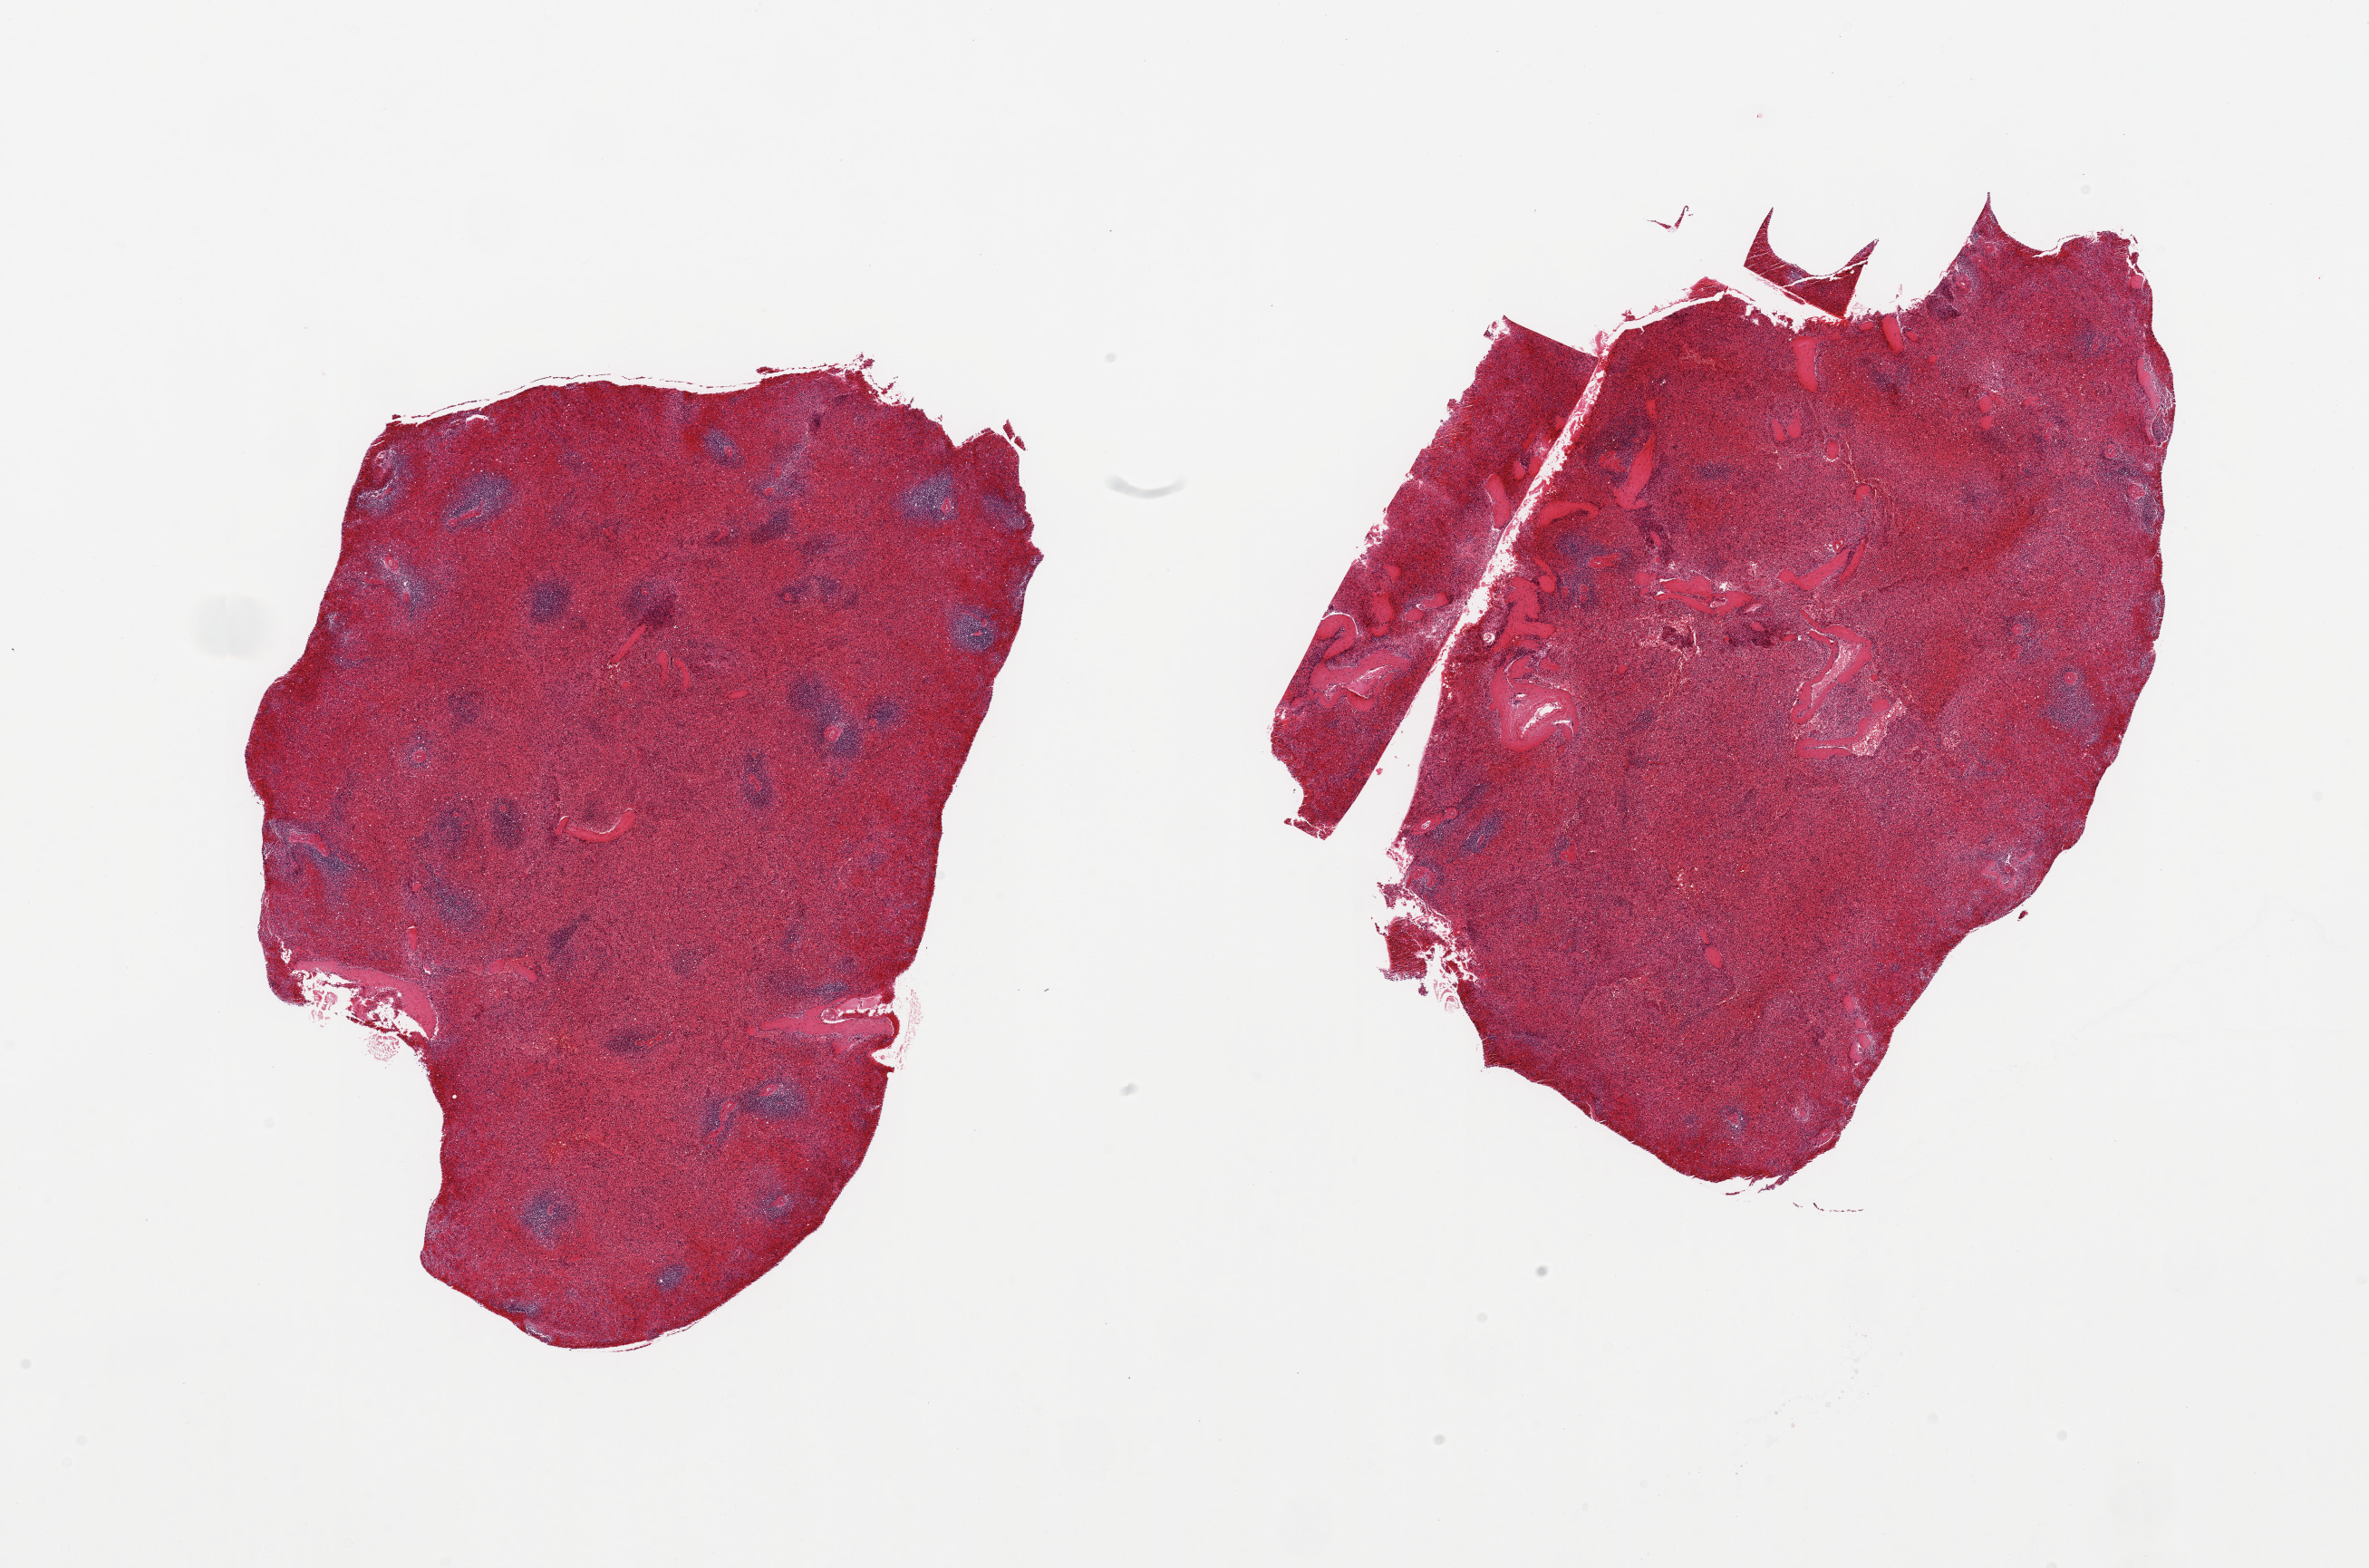
Digitized haematoxylin and eosin-stained section, brightfield, shown as a low-resolution overview of the whole scanned area (about 20.7 x 13.7 mm), PAXgene-fixed, paraffin-embedded tissue, sampled site (target tissue): spleen, donor tissue sample. Donor sex: male.
Reviewer comment on this tissue sample: 2 pieces; moderate congestion.